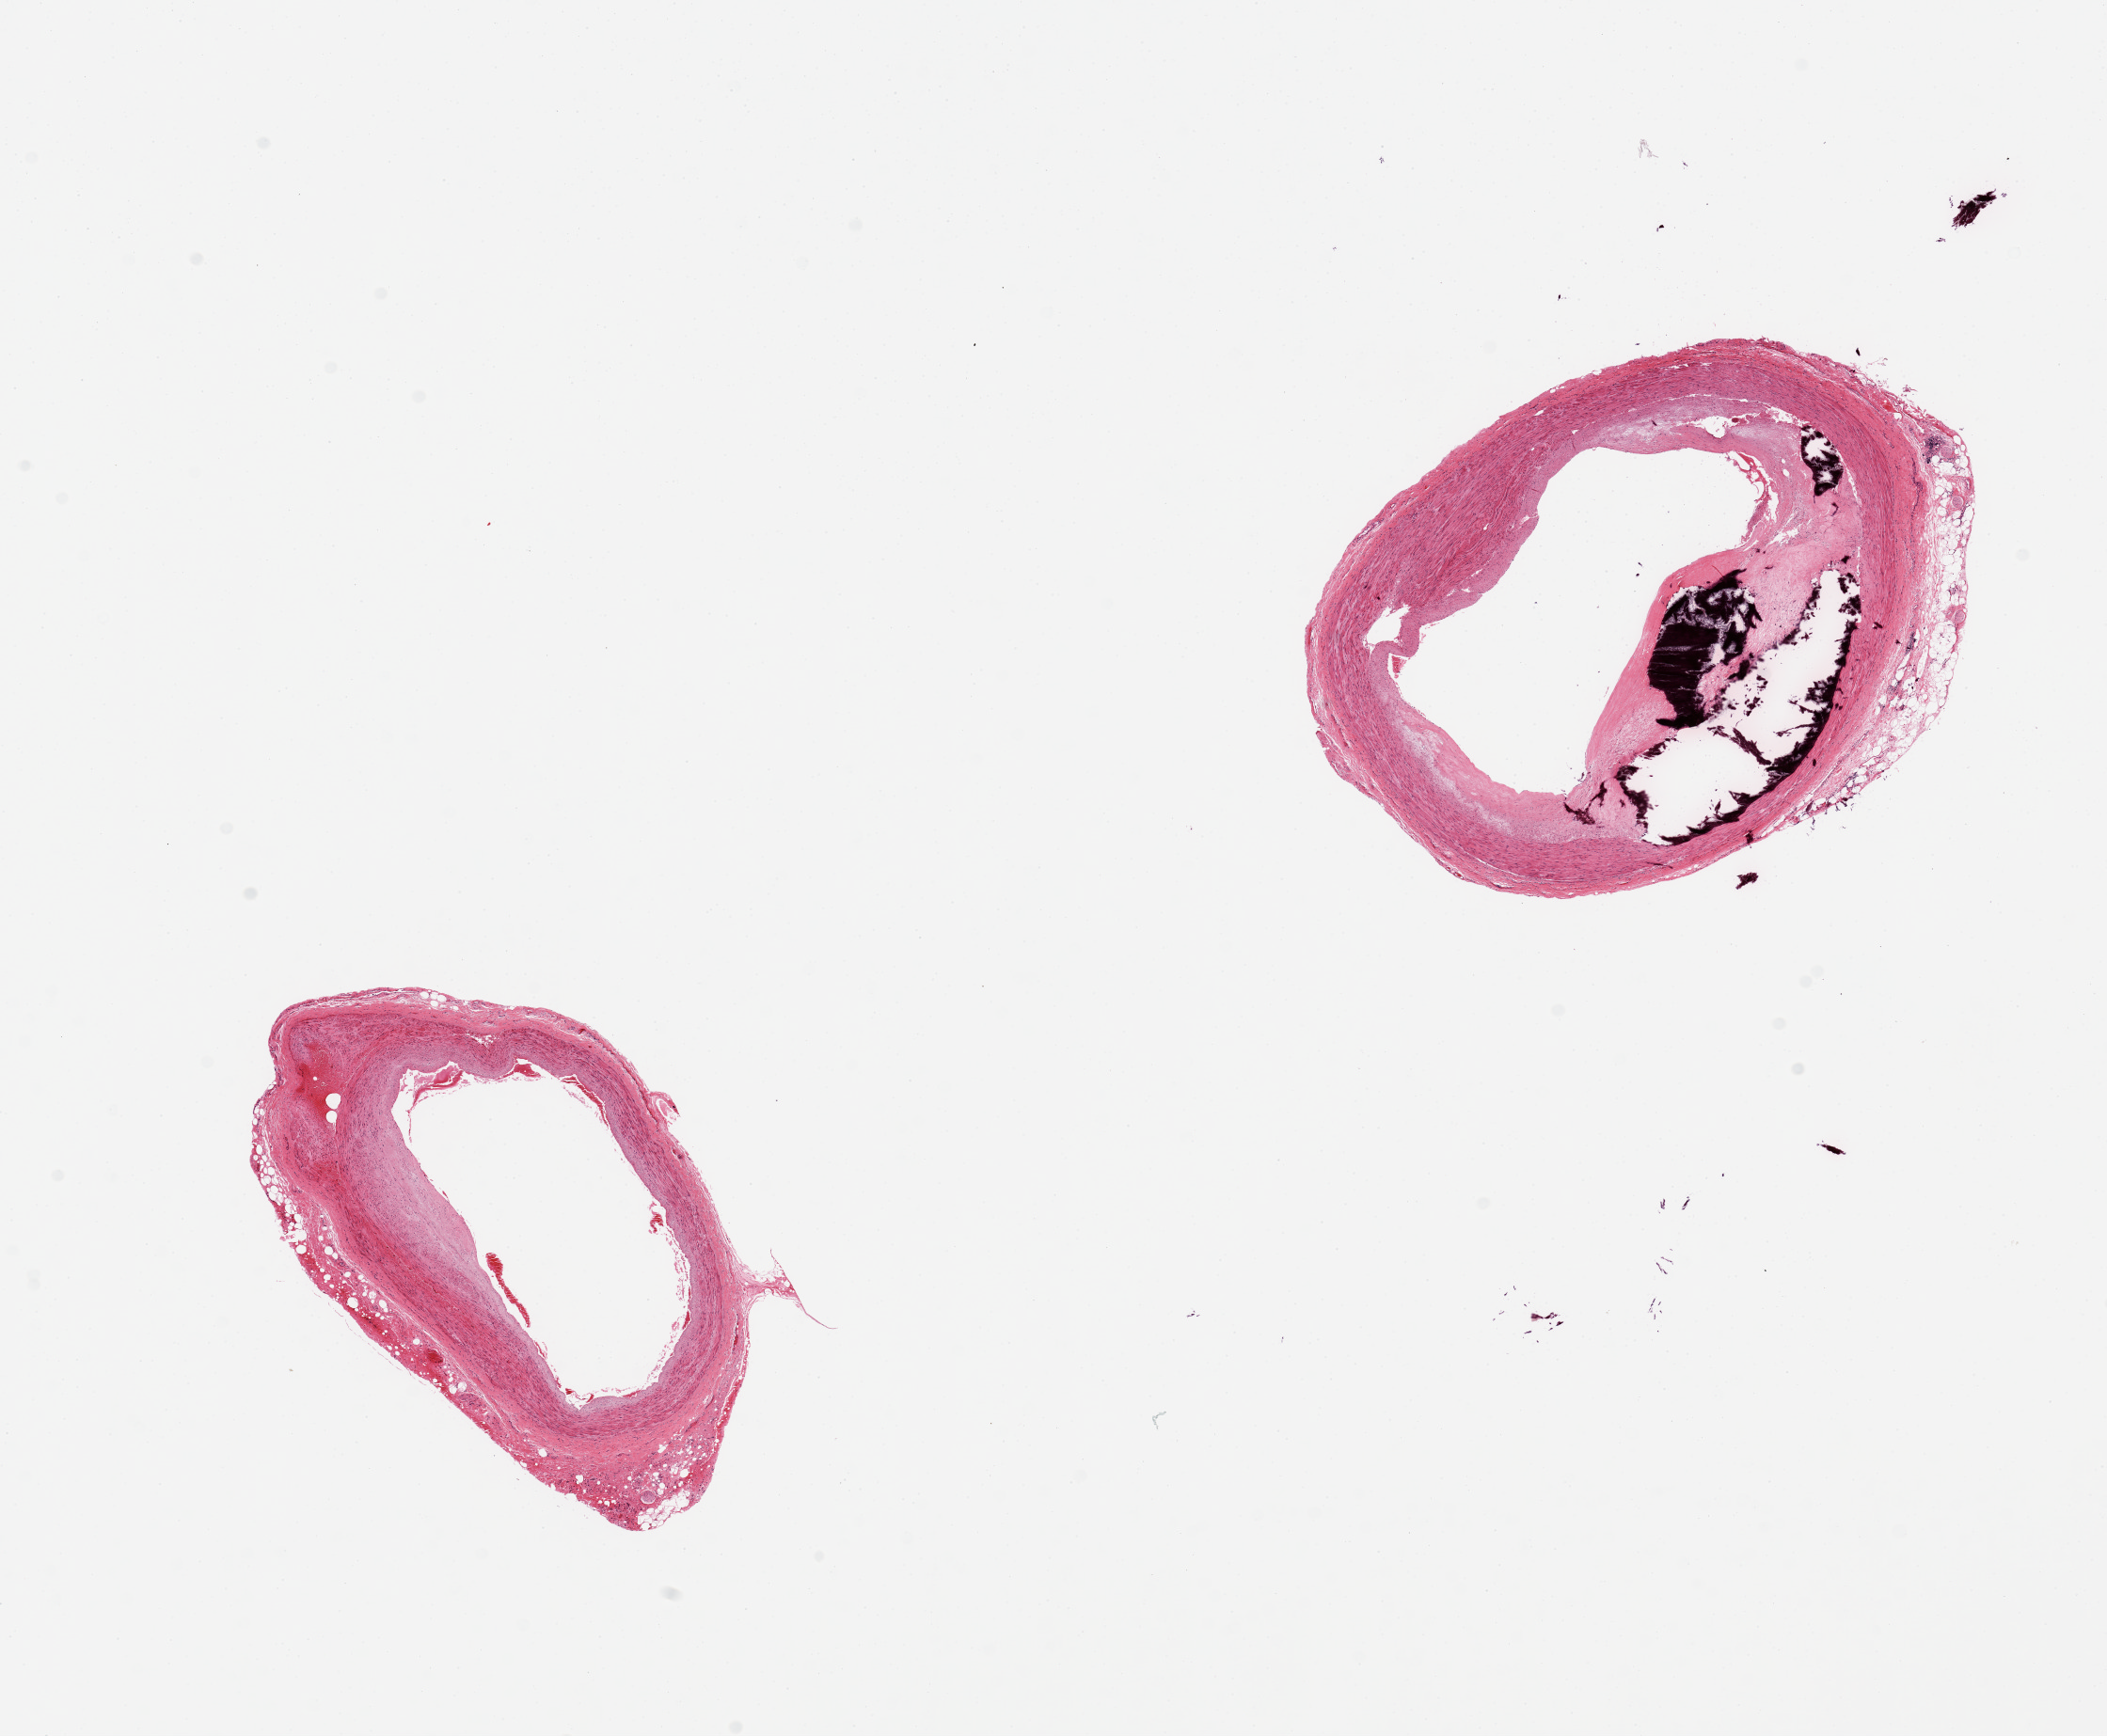
Digitized haematoxylin and eosin-stained section, shown as a low-resolution overview of the whole scanned area (about 17.7 x 14.6 mm), PAXgene-fixed, paraffin-embedded tissue, target tissue: coronary artery, tissue donor sample.
* review note (as recorded): 2 pieces, ~50% occlusive calcified atherosis; Trace adherent fat up to ~0.3mm, good specimens